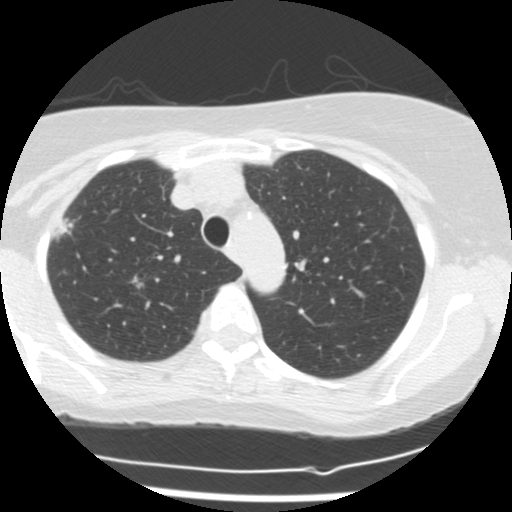
Low-dose screening chest CT, axial slice; first (baseline) screen; lung window (W 1500 / L -600 HU); standard (soft-tissue) reconstruction kernel (STANDARD); 120 kVp; 512 × 512 image matrix, field of view 300 × 300 mm. Female, age 58 years at enrolment. Former smoker at enrolment.
Expert-annotated lung lesion, box from (x=44, y=206) to (x=87, y=243) px. Reader record for this screening exam (exam-level; its link to the box is not recorded): non-calcified nodule or mass ≥4 mm, right upper lobe, 12 × 9 mm, spiculated (stellate) margins, soft tissue attenuation. Participant outcome: lung cancer diagnosed 21 days after this screen — adenocarcinoma, NOS, right upper lobe, moderately differentiated (G2), stage IA (AJCC 6th edition), 10 mm at pathology.